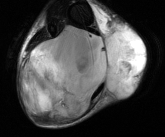
MRI of an extremity soft-tissue mass, one axial slice. Position 33 of 81 along the scan axis. T2-weighted fat-saturated. MR volume resampled by the dataset authors to the PET/CT grid (not the native acquisition matrix). 3.27 mm slice thickness. 165 × 137 image matrix. Male patient. Case-level facts recorded for this patient, not image findings: histological type: liposarcoma - round cell; grade: high; site of the primary tumour: right calf.
Annotated regions visible in this slice (expert contour drawn on MRI and transferred to this co-registered scan by the dataset authors):
- gross tumour volume (mass): box from (x=21, y=25) to (x=145, y=120) px